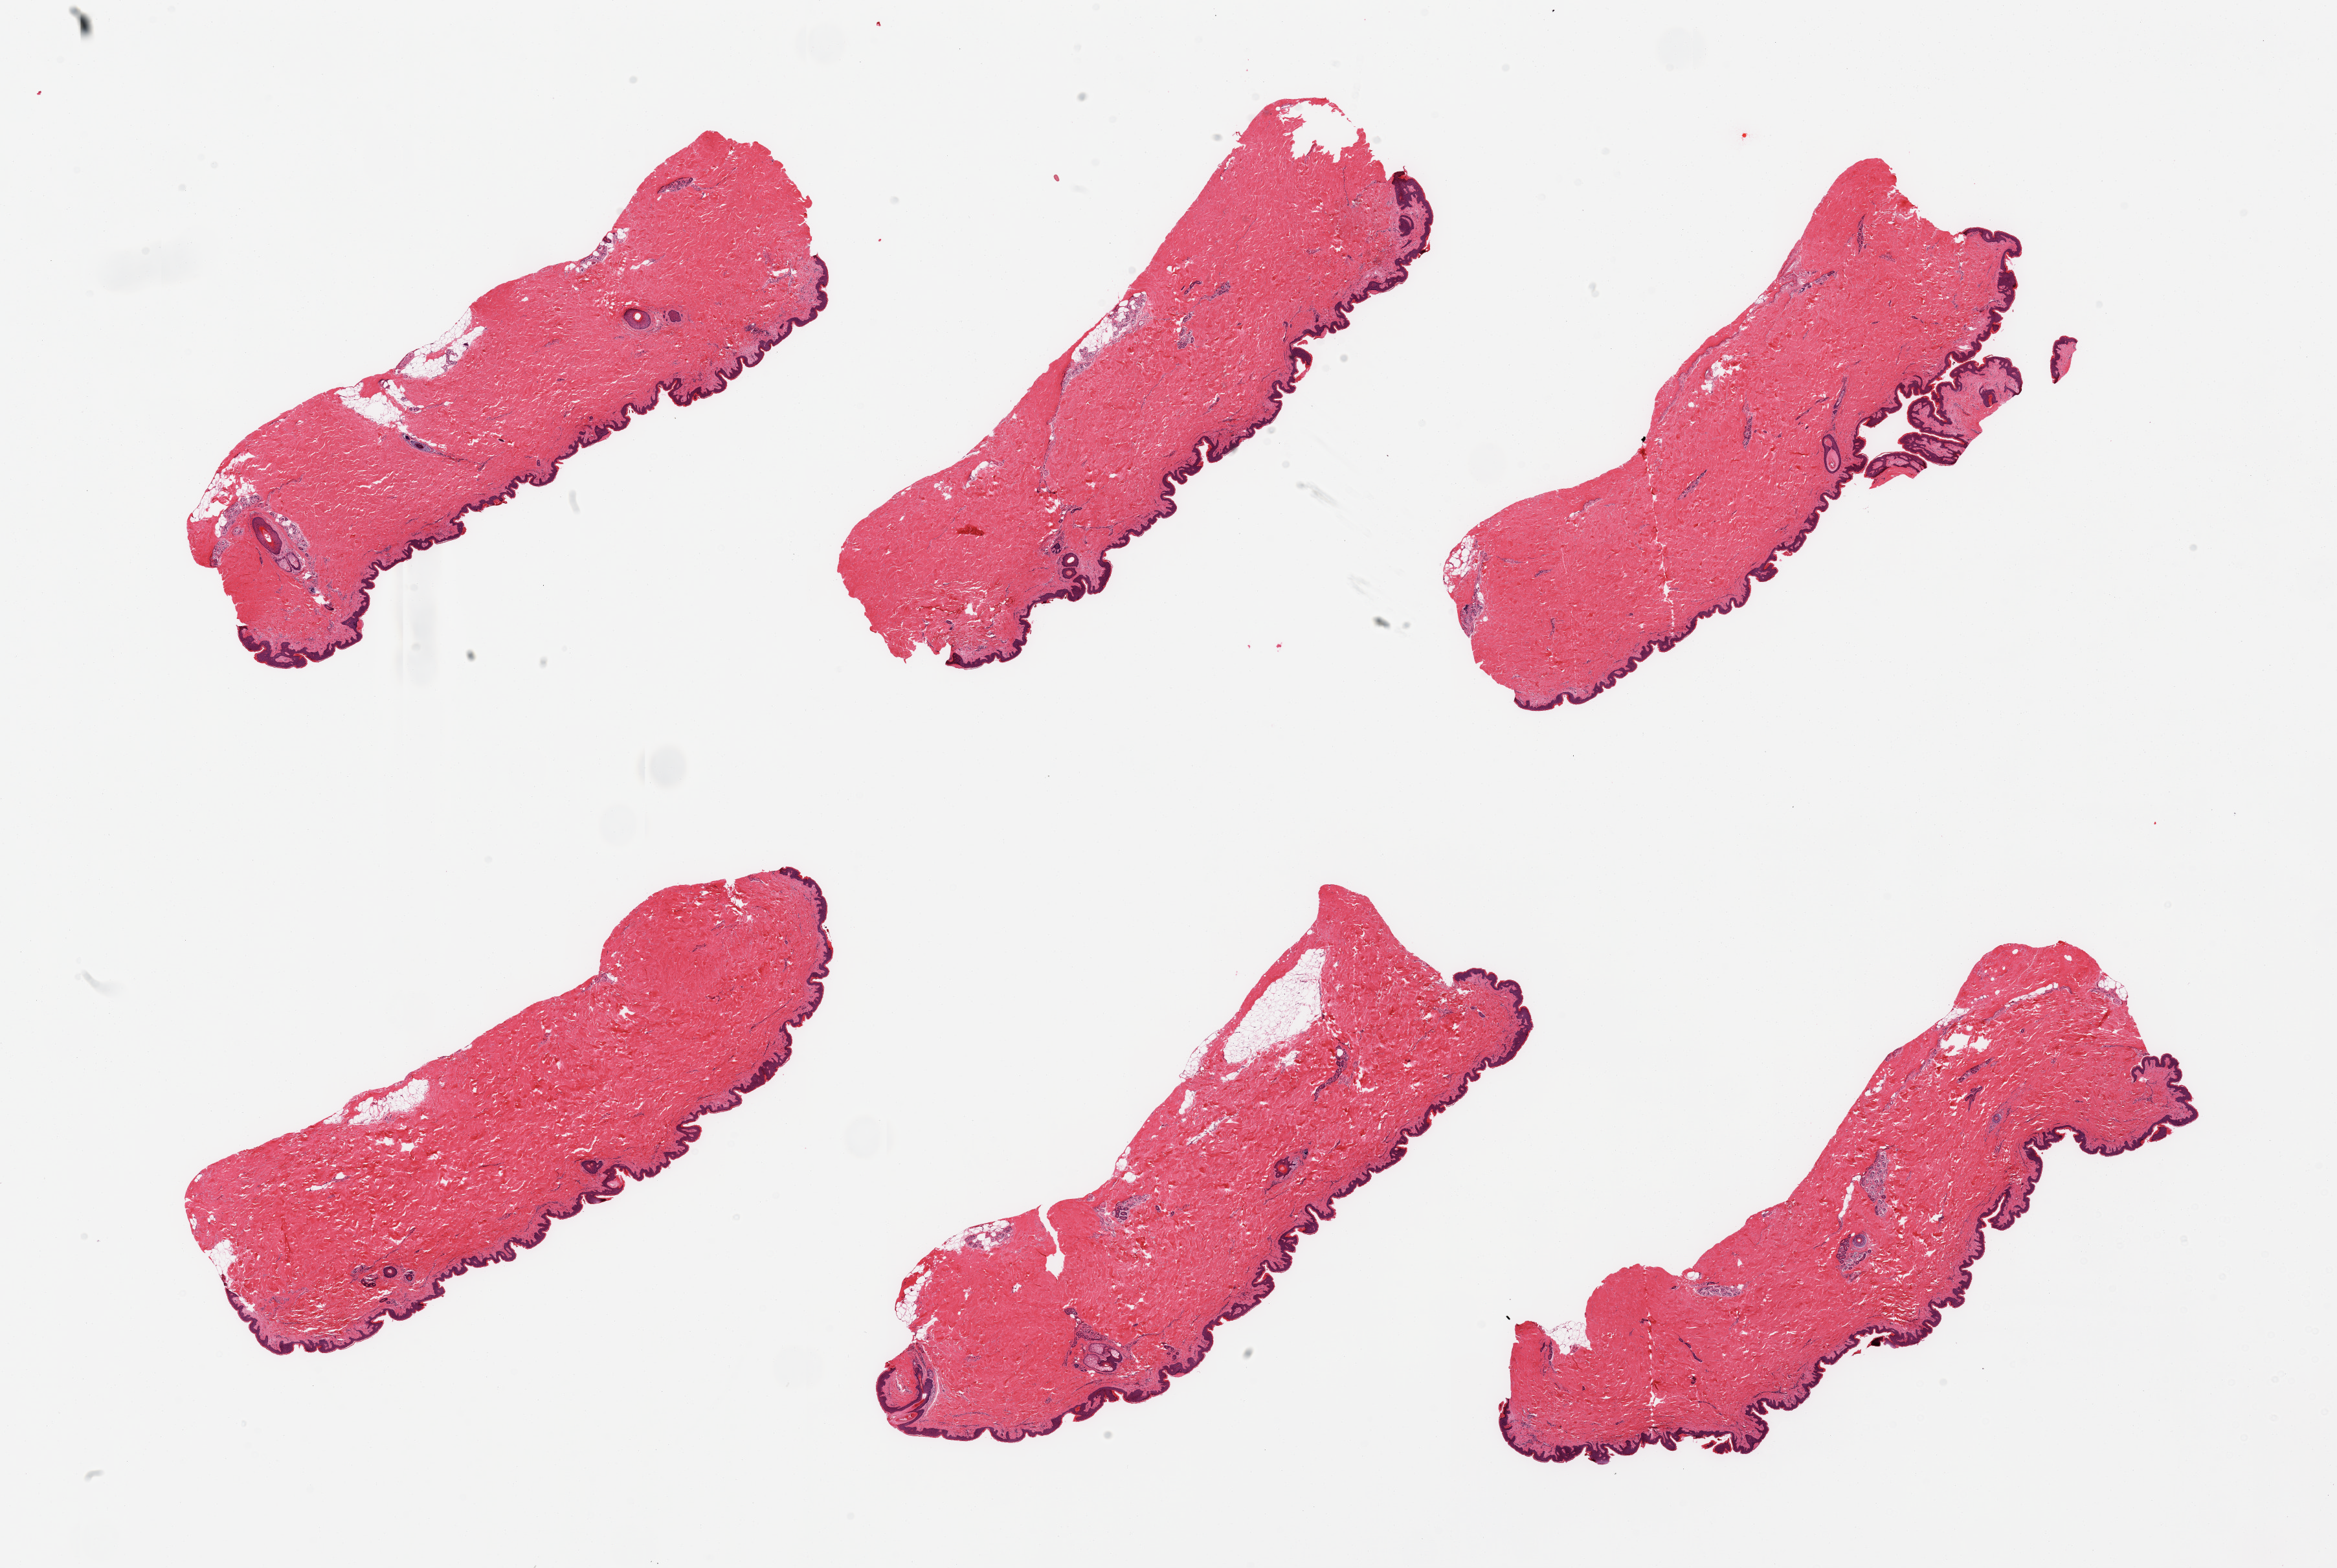
Whole-slide image, H&E stain, whole scanned area (about 28.5 x 19.2 mm, slide scanned at 20x) shown as a low-resolution overview. PAXgene-fixed, paraffin-embedded tissue. Section of skin of suprapubic region (target tissue). Tissue donor sample.
Reviewer comment on this tissue sample: 6 pieces, no dermal fat; squamous epithlium is ~60 microns.